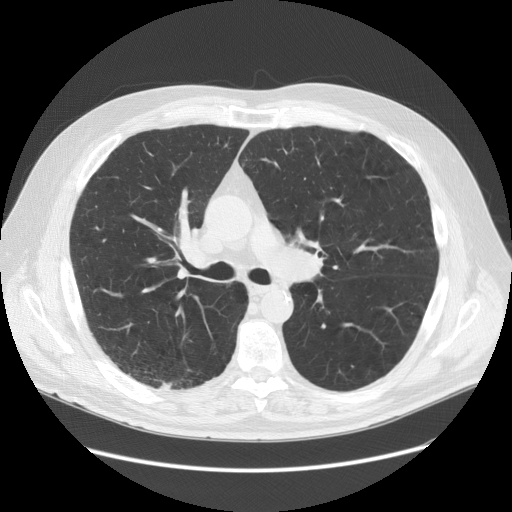
Low-dose screening chest CT, one axial slice. Slice 90 of 149 in the series (ordered by position). Reconstruction kernel STANDARD. 120 kVp. Lung window (W 1500 / L -600 HU). 512 × 512 image matrix.
Annotated regions visible in this slice (manually delineated by an expert):
- lesion 1 (tumor, lower lobe of right lung): bounding box <159,382,172,389> (left, top, right, bottom; pixels)